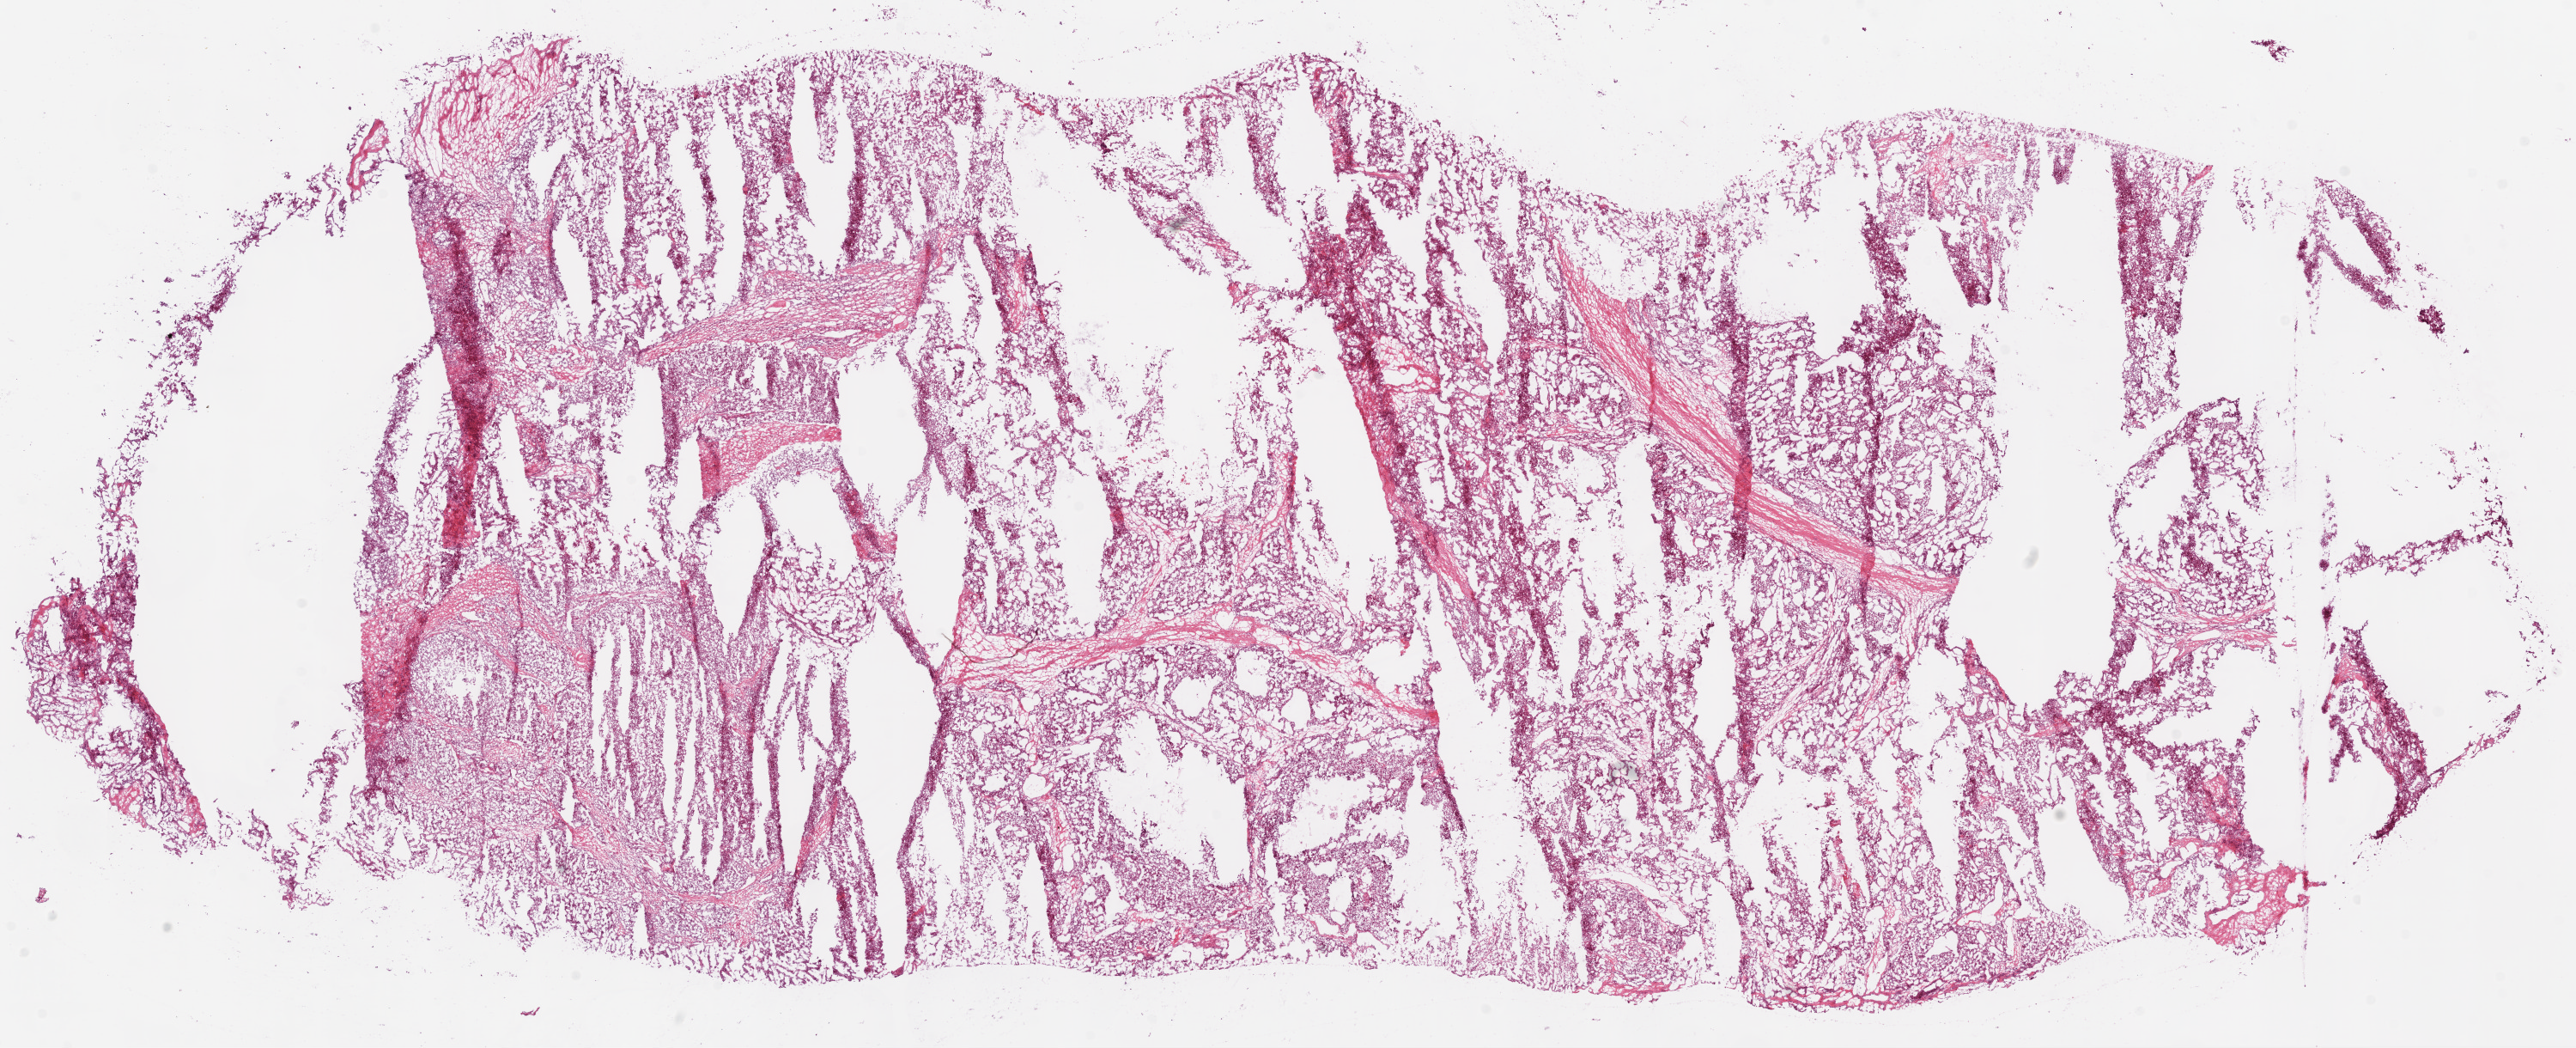
Whole-slide histology image, Hematoxylin and eosin (H&E) stained — shown as a low-resolution overview of the whole scanned area (about 24.1 x 9.8 mm, slide scanned at 20x), frozen section, kidney, primary tumour sample. Female patient; age at initial diagnosis 46 years.
Diagnosis: Clear cell adenocarcinoma, NOS.